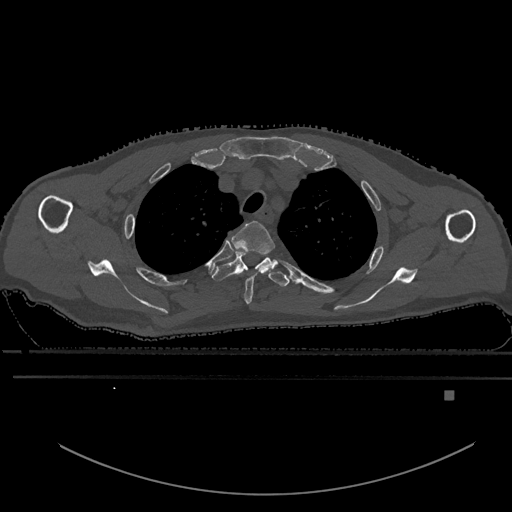
CT including the spine, one axial slice; slice 471 of 969 in the series (ordered by position); bone window (W 1800 / L 400 HU); 0.5 mm slice thickness; 512 × 512 image matrix, field of view 456 × 456 mm. Patient: male, 82 years. From the clinical record (not read from this slice): primary cancer: prostate; vertebrae with lytic lesions (as recorded): T11, T9, T8, T2.
Annotated regions visible in this slice (semi-automatically segmented with operator editing):
- T2 vertebra: box from (x=231, y=221) to (x=275, y=304) px
- T3 vertebra: (x=212, y=251)–(x=289, y=287)